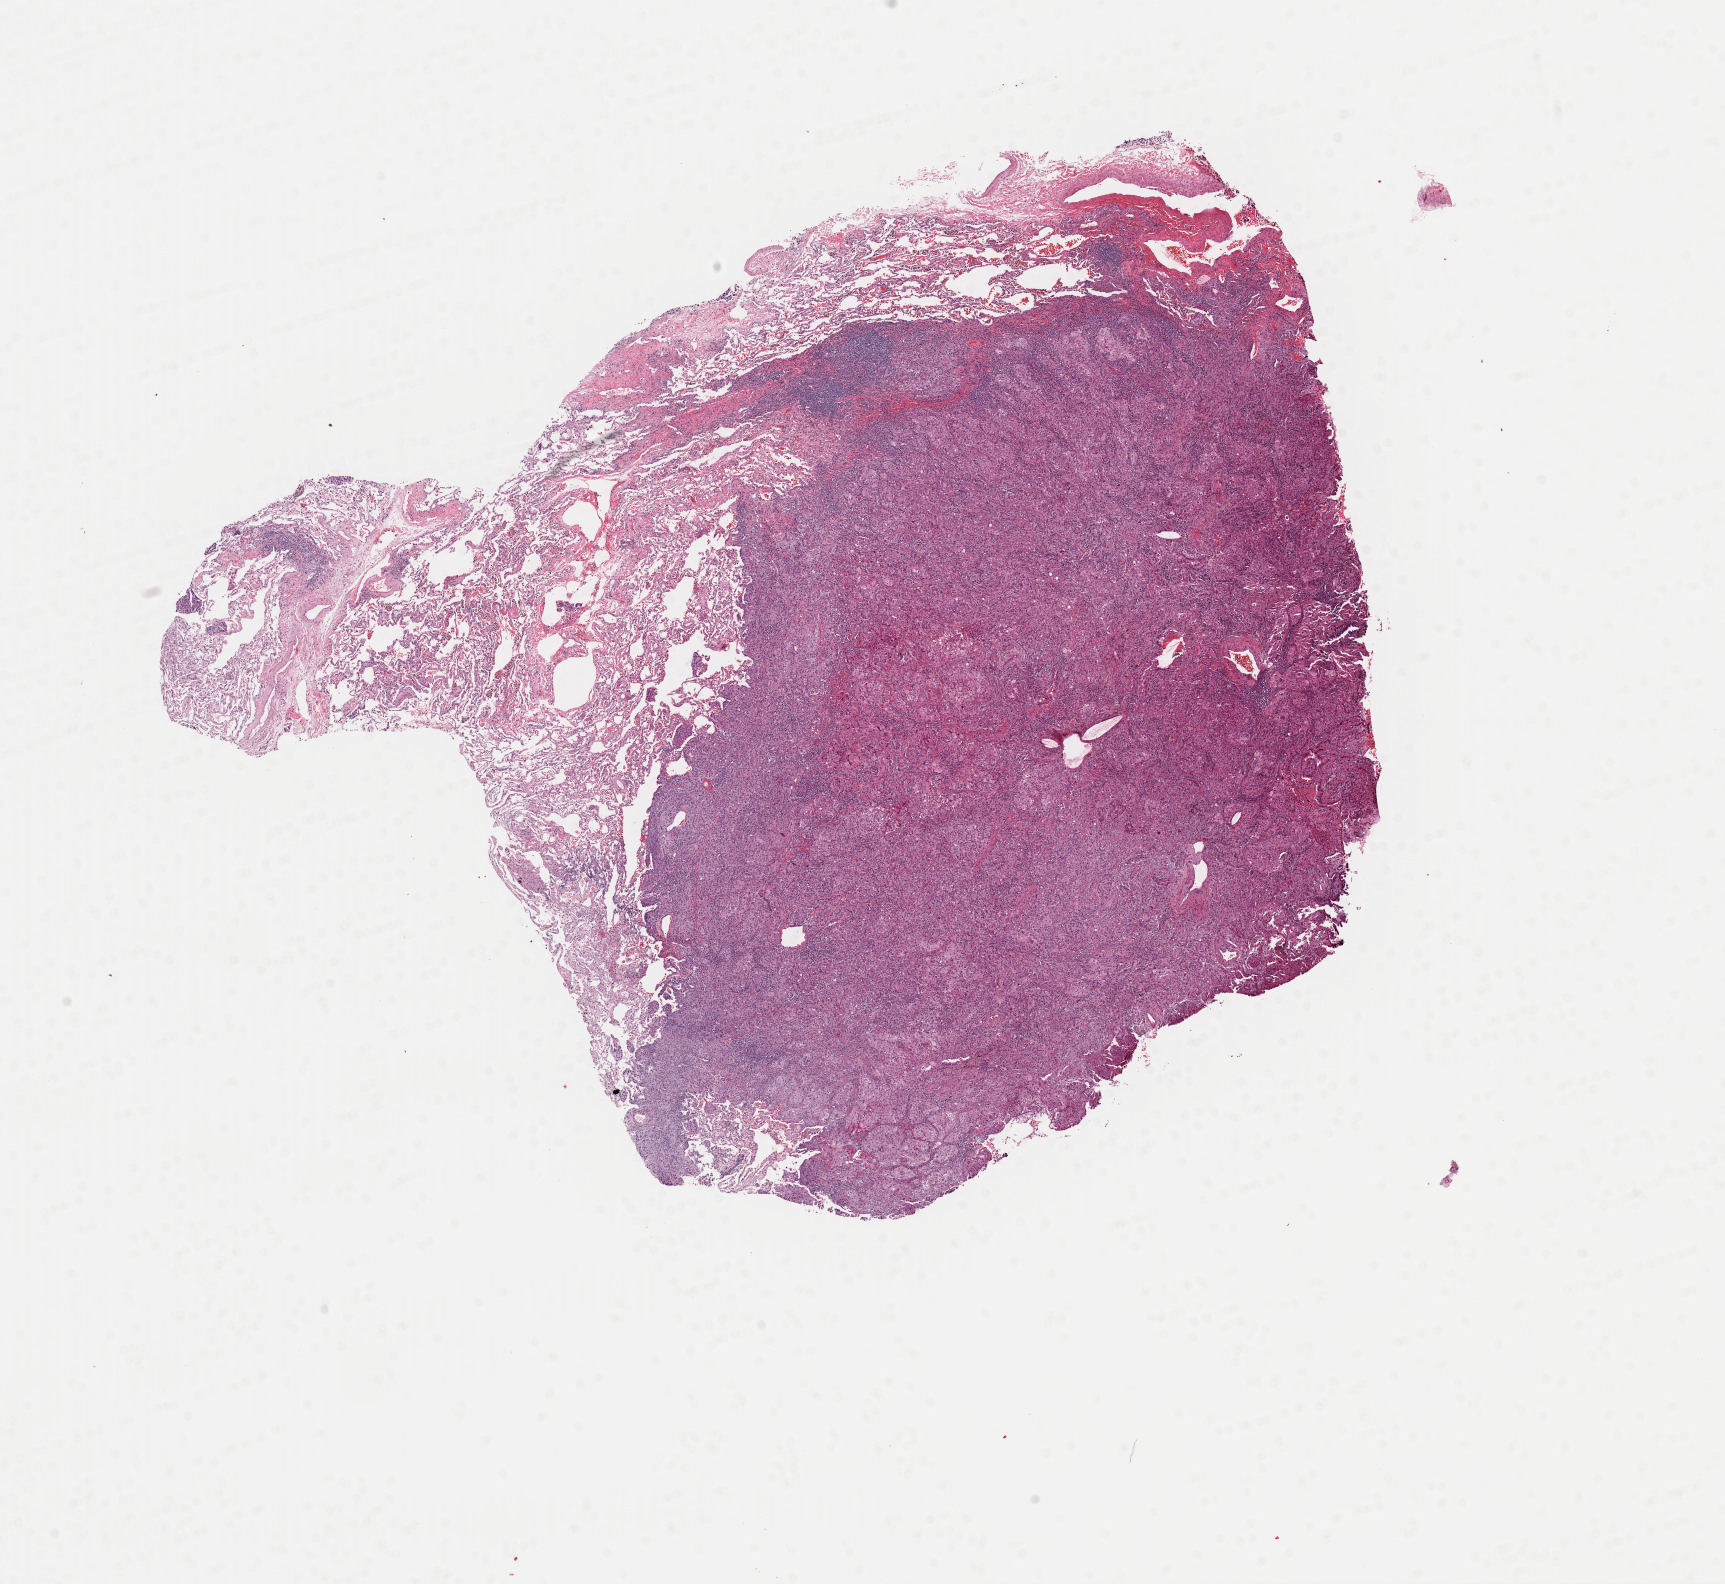
Digitized H&E-stained tissue section (whole slide), low-resolution overview of the scanned area, about 13.6 x 12.5 mm (acquisition: 40x scan), frozen section, primary tumour sample from the lung. Patient: male, age at initial diagnosis 59 years. Slide review estimates, as recorded: tumour cells 75%, tumour nuclei 75%, normal cells 3%, stromal cells 21%, necrosis 1%. Inflammatory infiltration, as recorded: lymphocyte infiltration 7%, monocyte infiltration 2%, neutrophil infiltration 3%.
- AJCC pathologic stage: IB
- histologic diagnosis: Adenocarcinoma, NOS (upper lobe, lung)